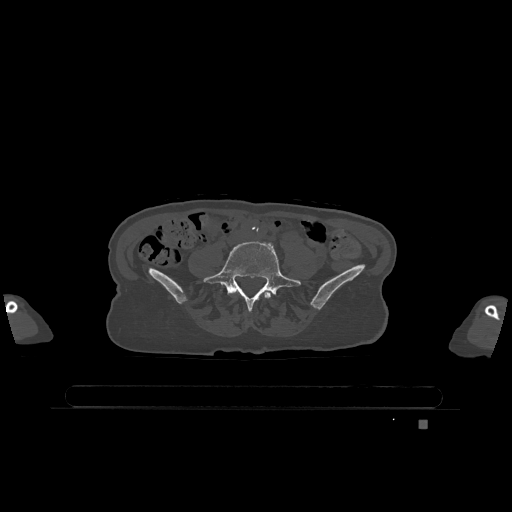
CT including the spine, one axial slice; position 249 of 1317 along the scan axis; bone window (W 1800 / L 400 HU); 0.5 mm slice thickness; 512 × 512 image matrix, field of view 500 × 500 mm. Patient: female, 74 years. Case-level facts recorded for this patient, not image findings: primary cancer: lung; vertebrae with lytic lesions (as recorded): T1, T4, T5, T6, L4, L5.
Annotated regions visible in this slice (semi-automatically segmented with operator editing):
- L4 vertebra: bounding box [x1, y1, x2, y2] px = [263, 292, 271, 299]
- L5 vertebra: [204, 241, 301, 311]